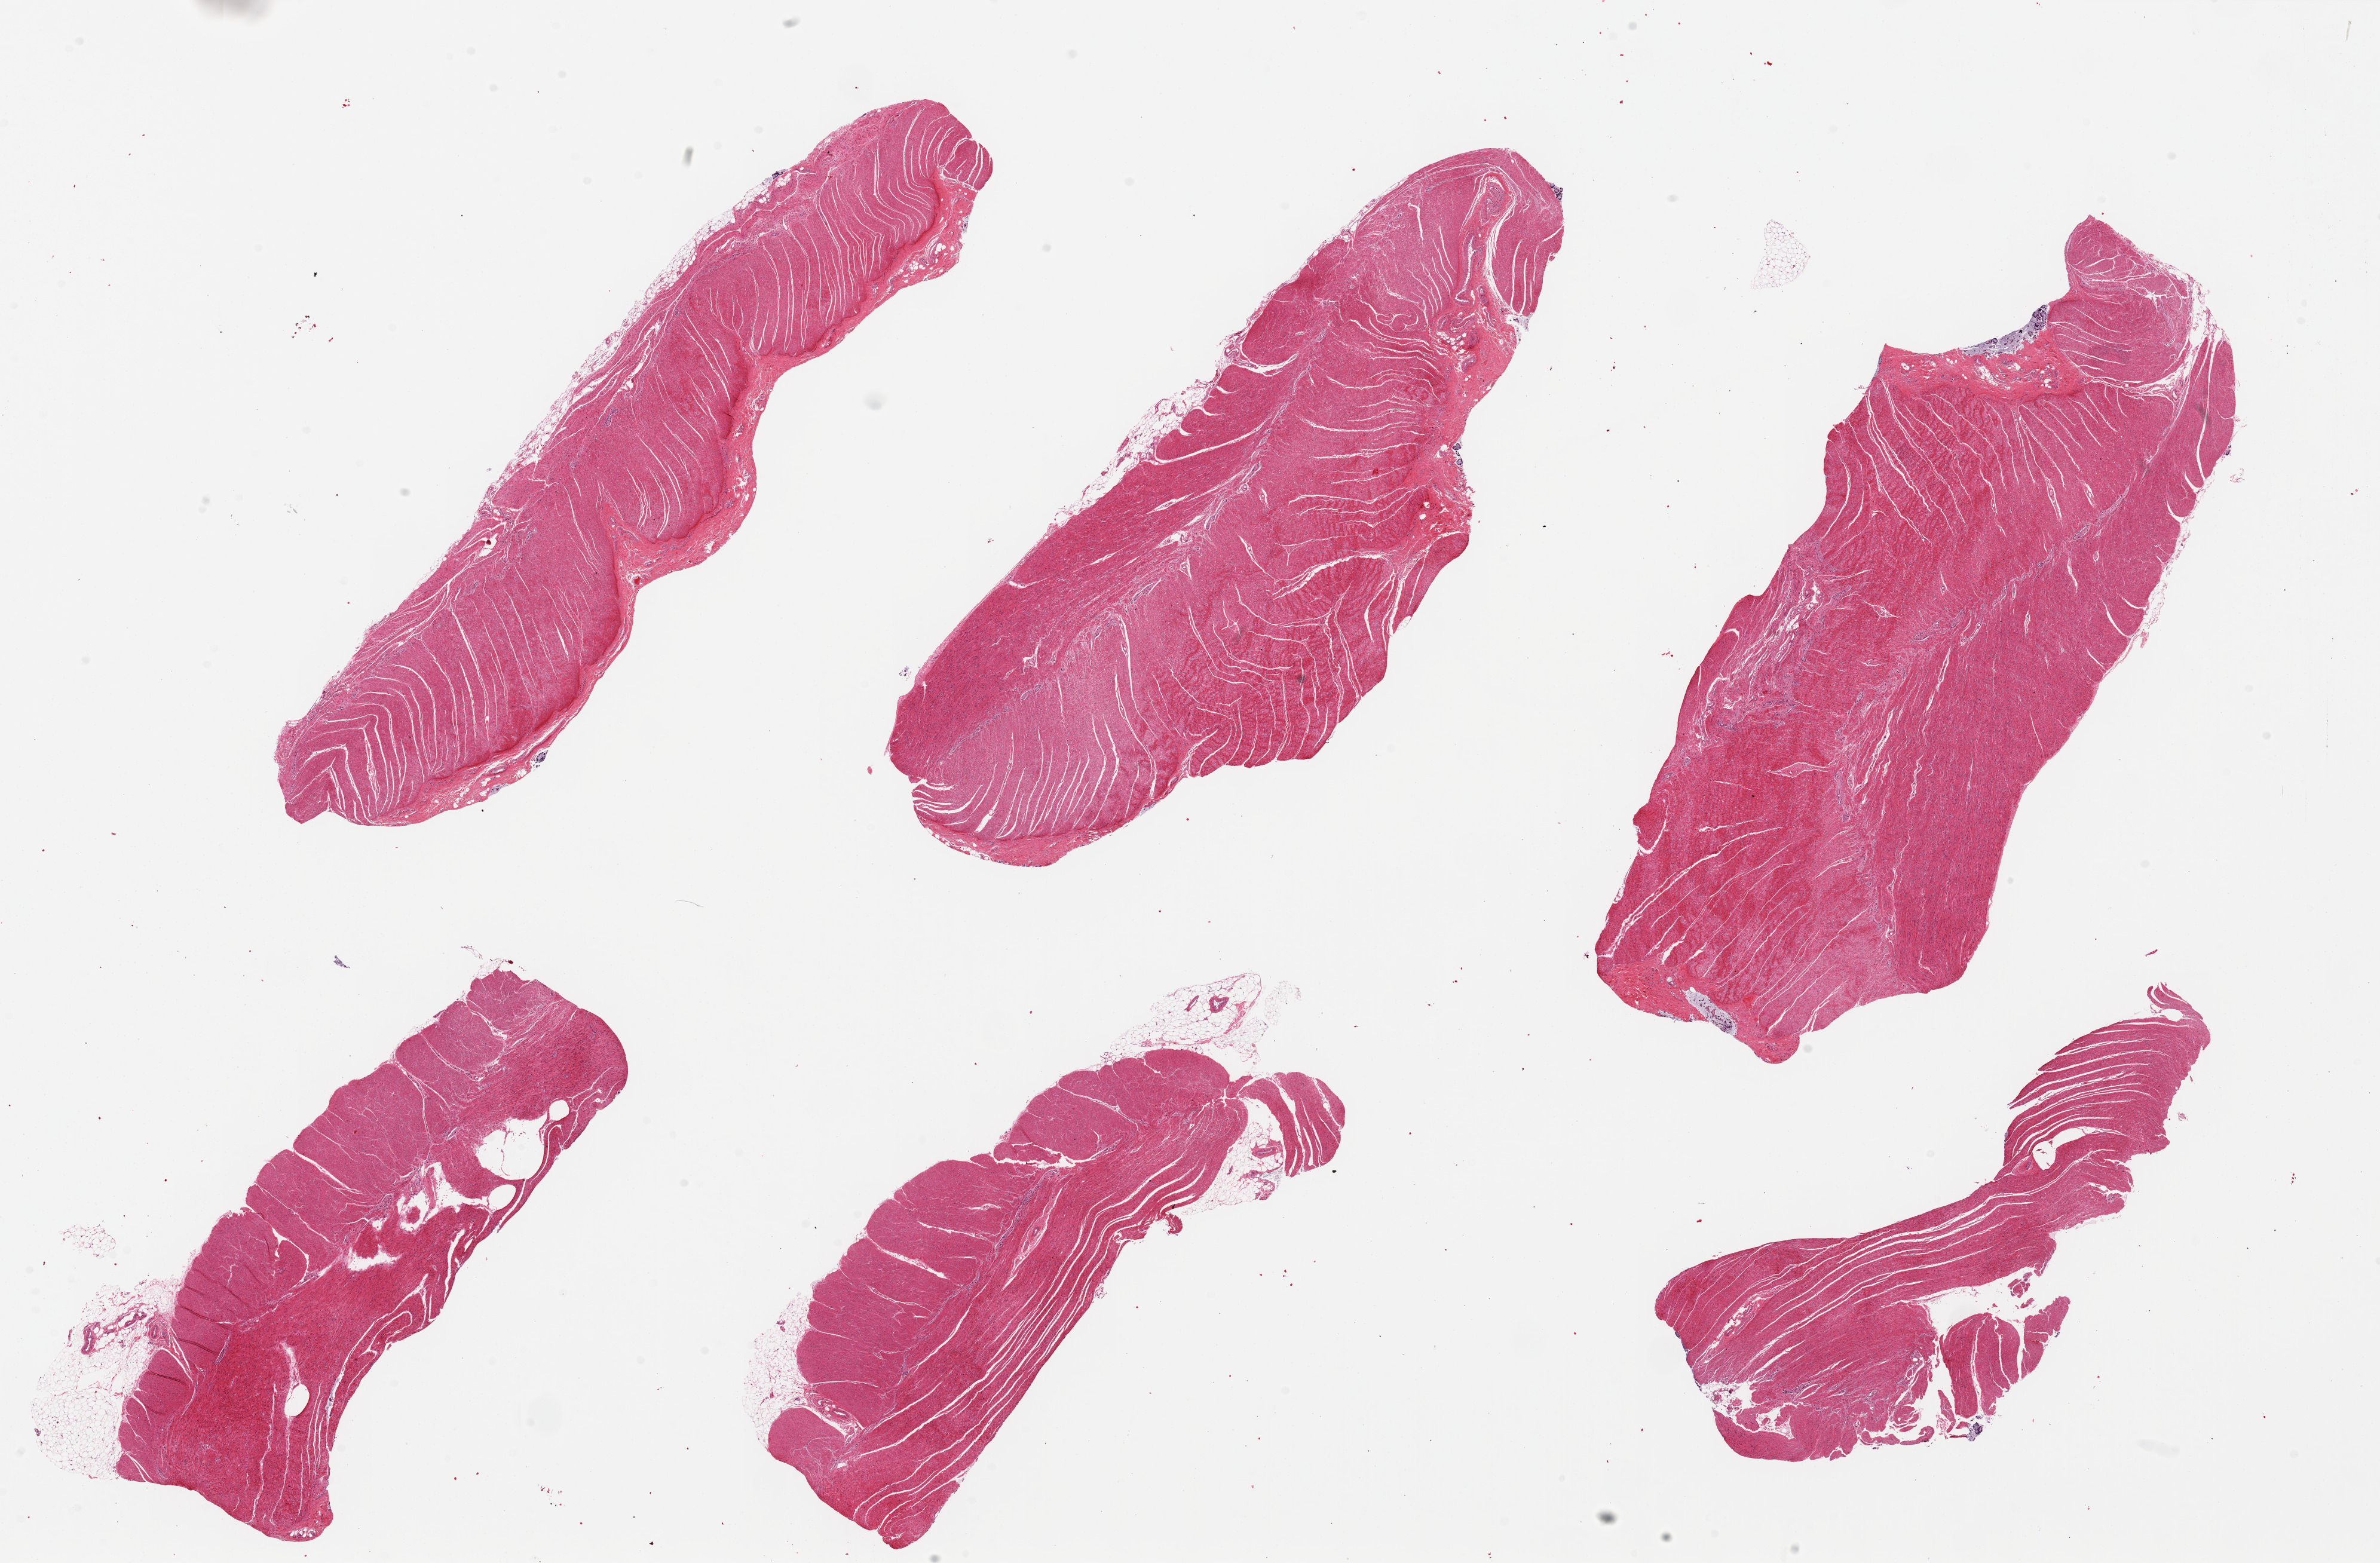
Whole-slide image, haematoxylin and eosin stain, shown as a low-resolution overview of the whole scanned area (about 31.5 x 20.7 mm, from a 20x scan); PAXgene-fixed paraffin-embedded (PFPE) section; target tissue: sigmoid colon; donor tissue sample. Donor: male.
Review note (as recorded): 6 pieces ~12x4mm. All muscularis propria, excellent specimen.